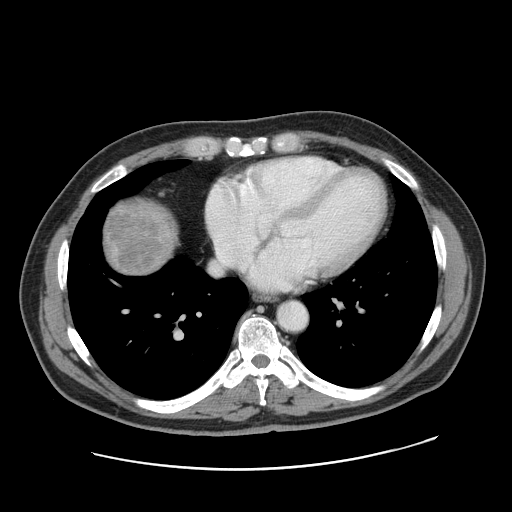
Contrast-enhanced abdominal CT, one axial slice; slice 162 of 178 in the series (ordered by position); 120 kVp; intravenous contrast given; soft-tissue window (W 400 / L 40 HU); 512 × 512 image matrix, field of view 403 × 403 mm. Male patient, age 63 years. Case-level facts recorded for this patient, not image findings: diagnosis: colorectal cancer liver metastases, imaged before liver resection; multiple liver metastases: yes; largest metastasis: 8 cm.
Structures marked on this image (manually delineated by an expert):
- liver: bounding box <102,202,175,276> (left, top, right, bottom; pixels)
- liver metastasis: <106,203,164,274>